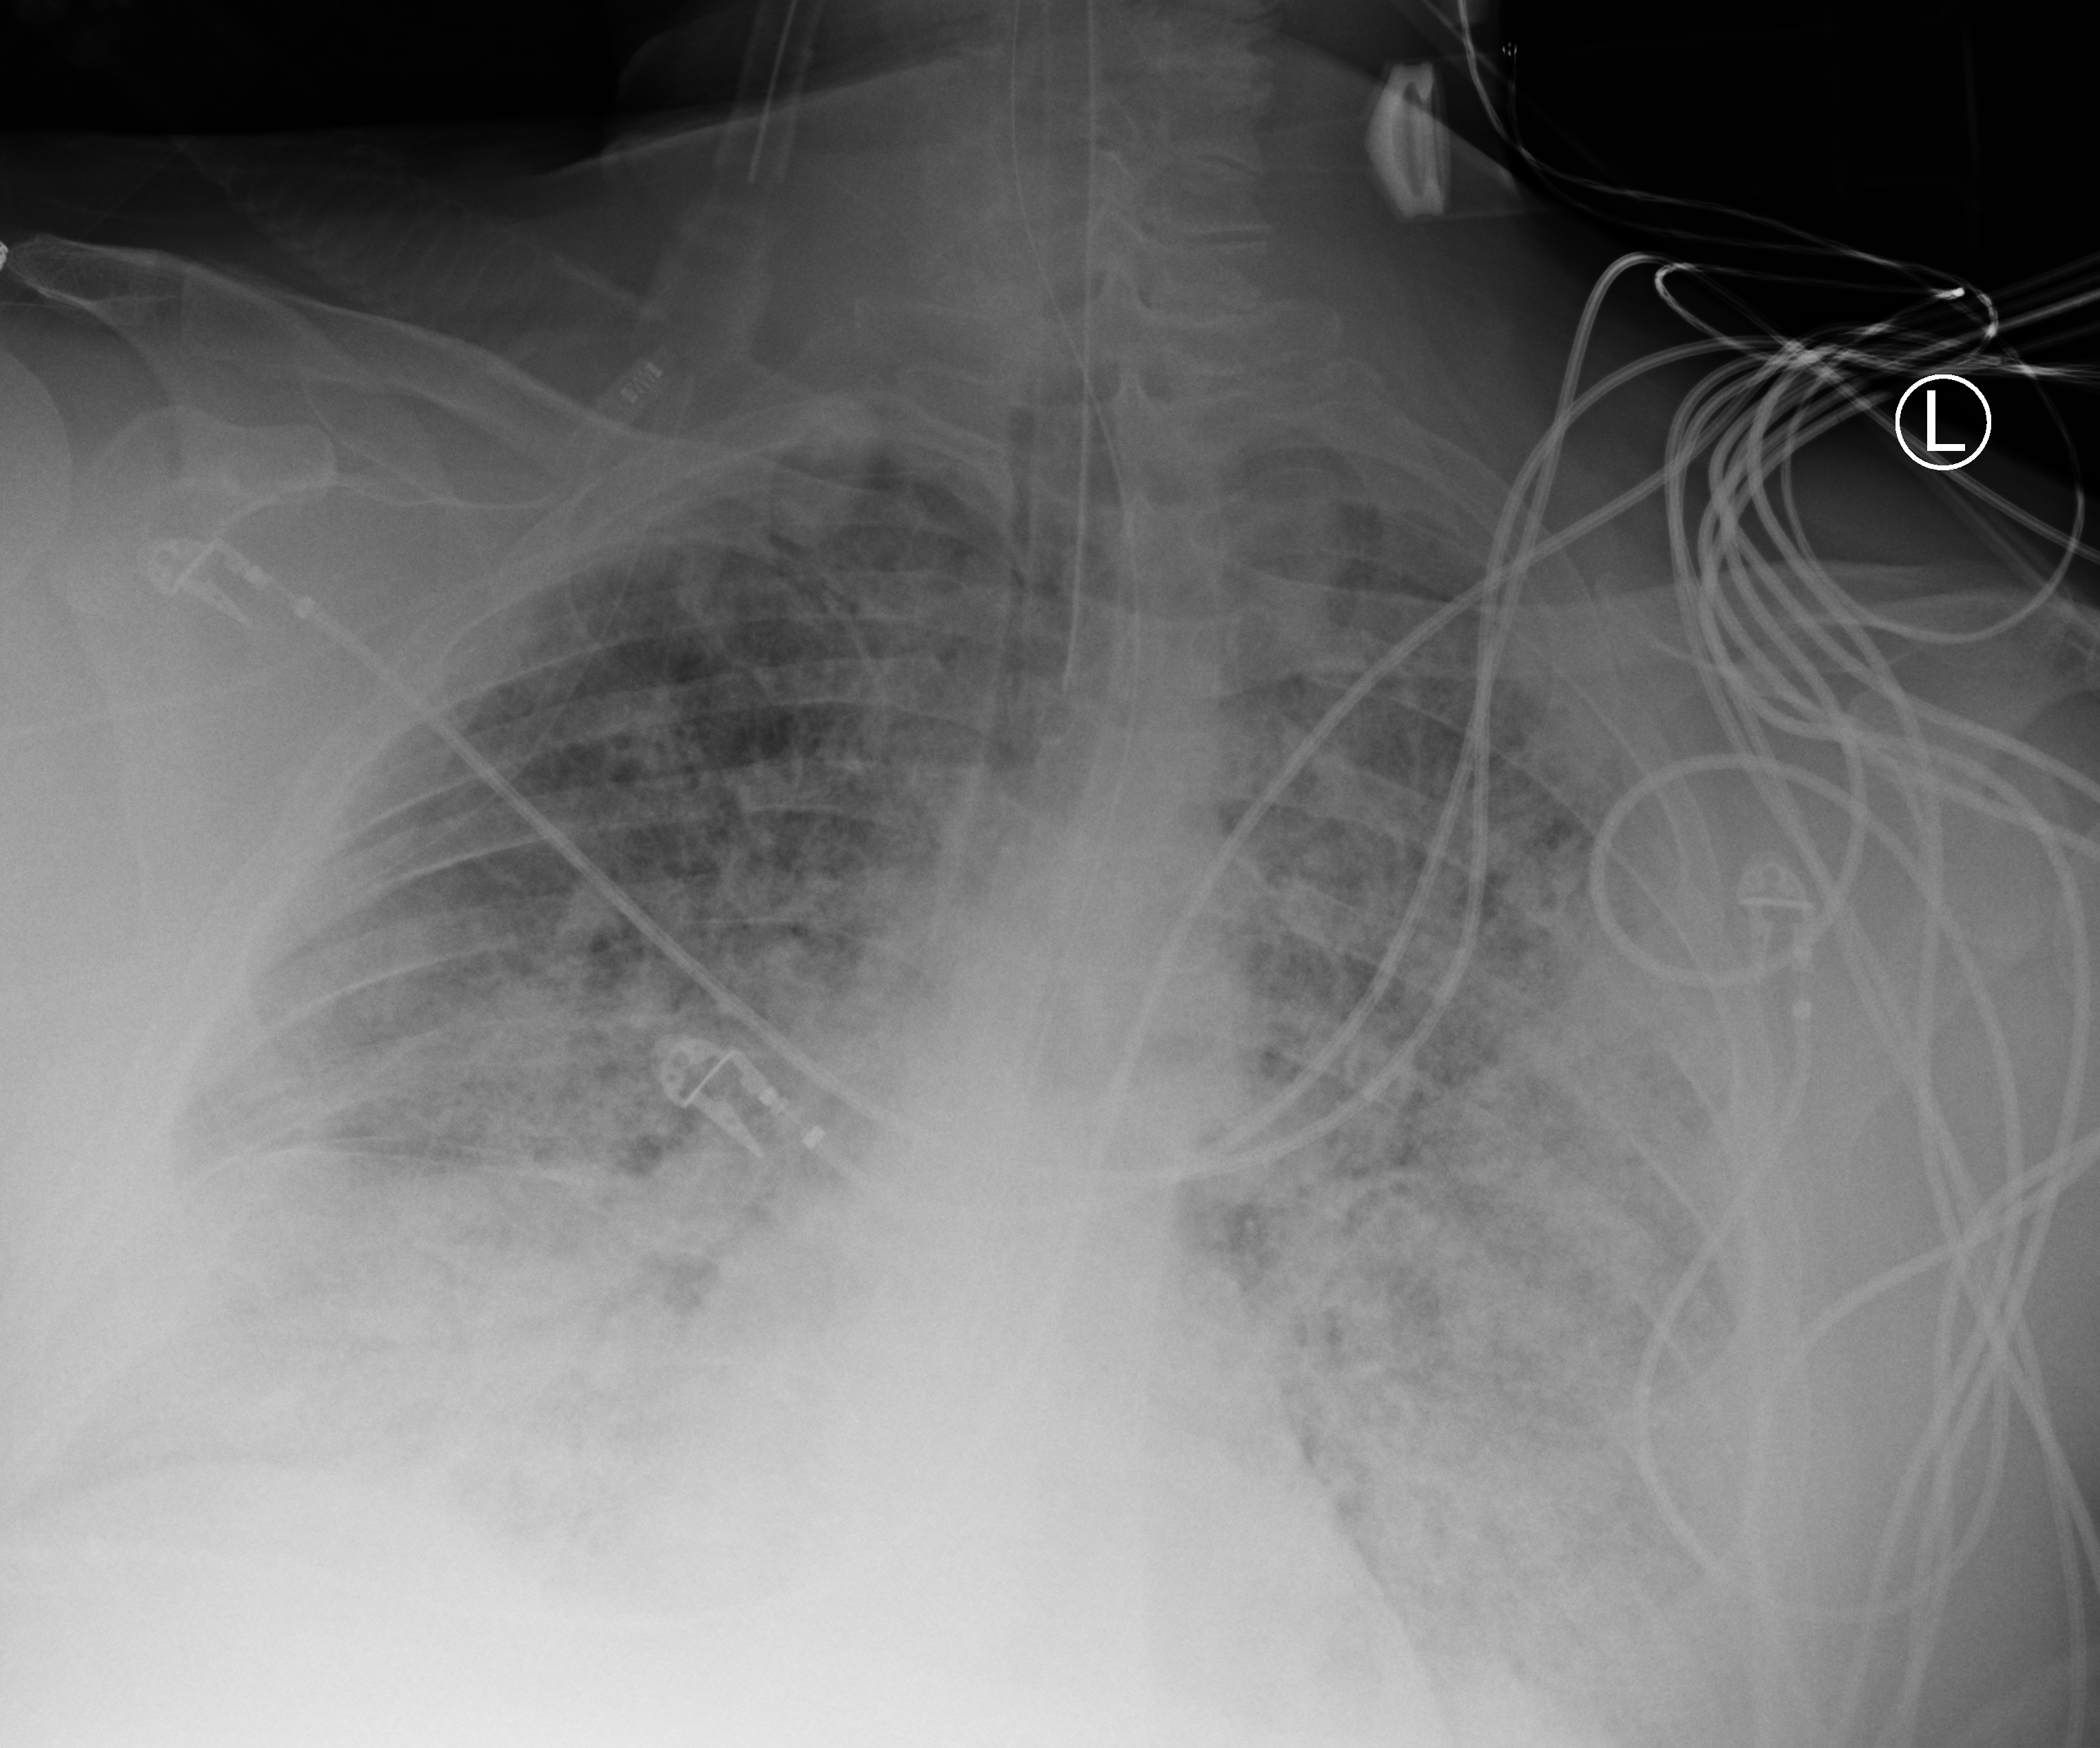
Bedside chest radiograph (computed radiography). Patient hospitalised with COVID-19; male, aged 60–74 years.
Hospital-stay facts (about this admission, not read from this image; timing relative to this image not recorded): hypertension (admission record): yes.